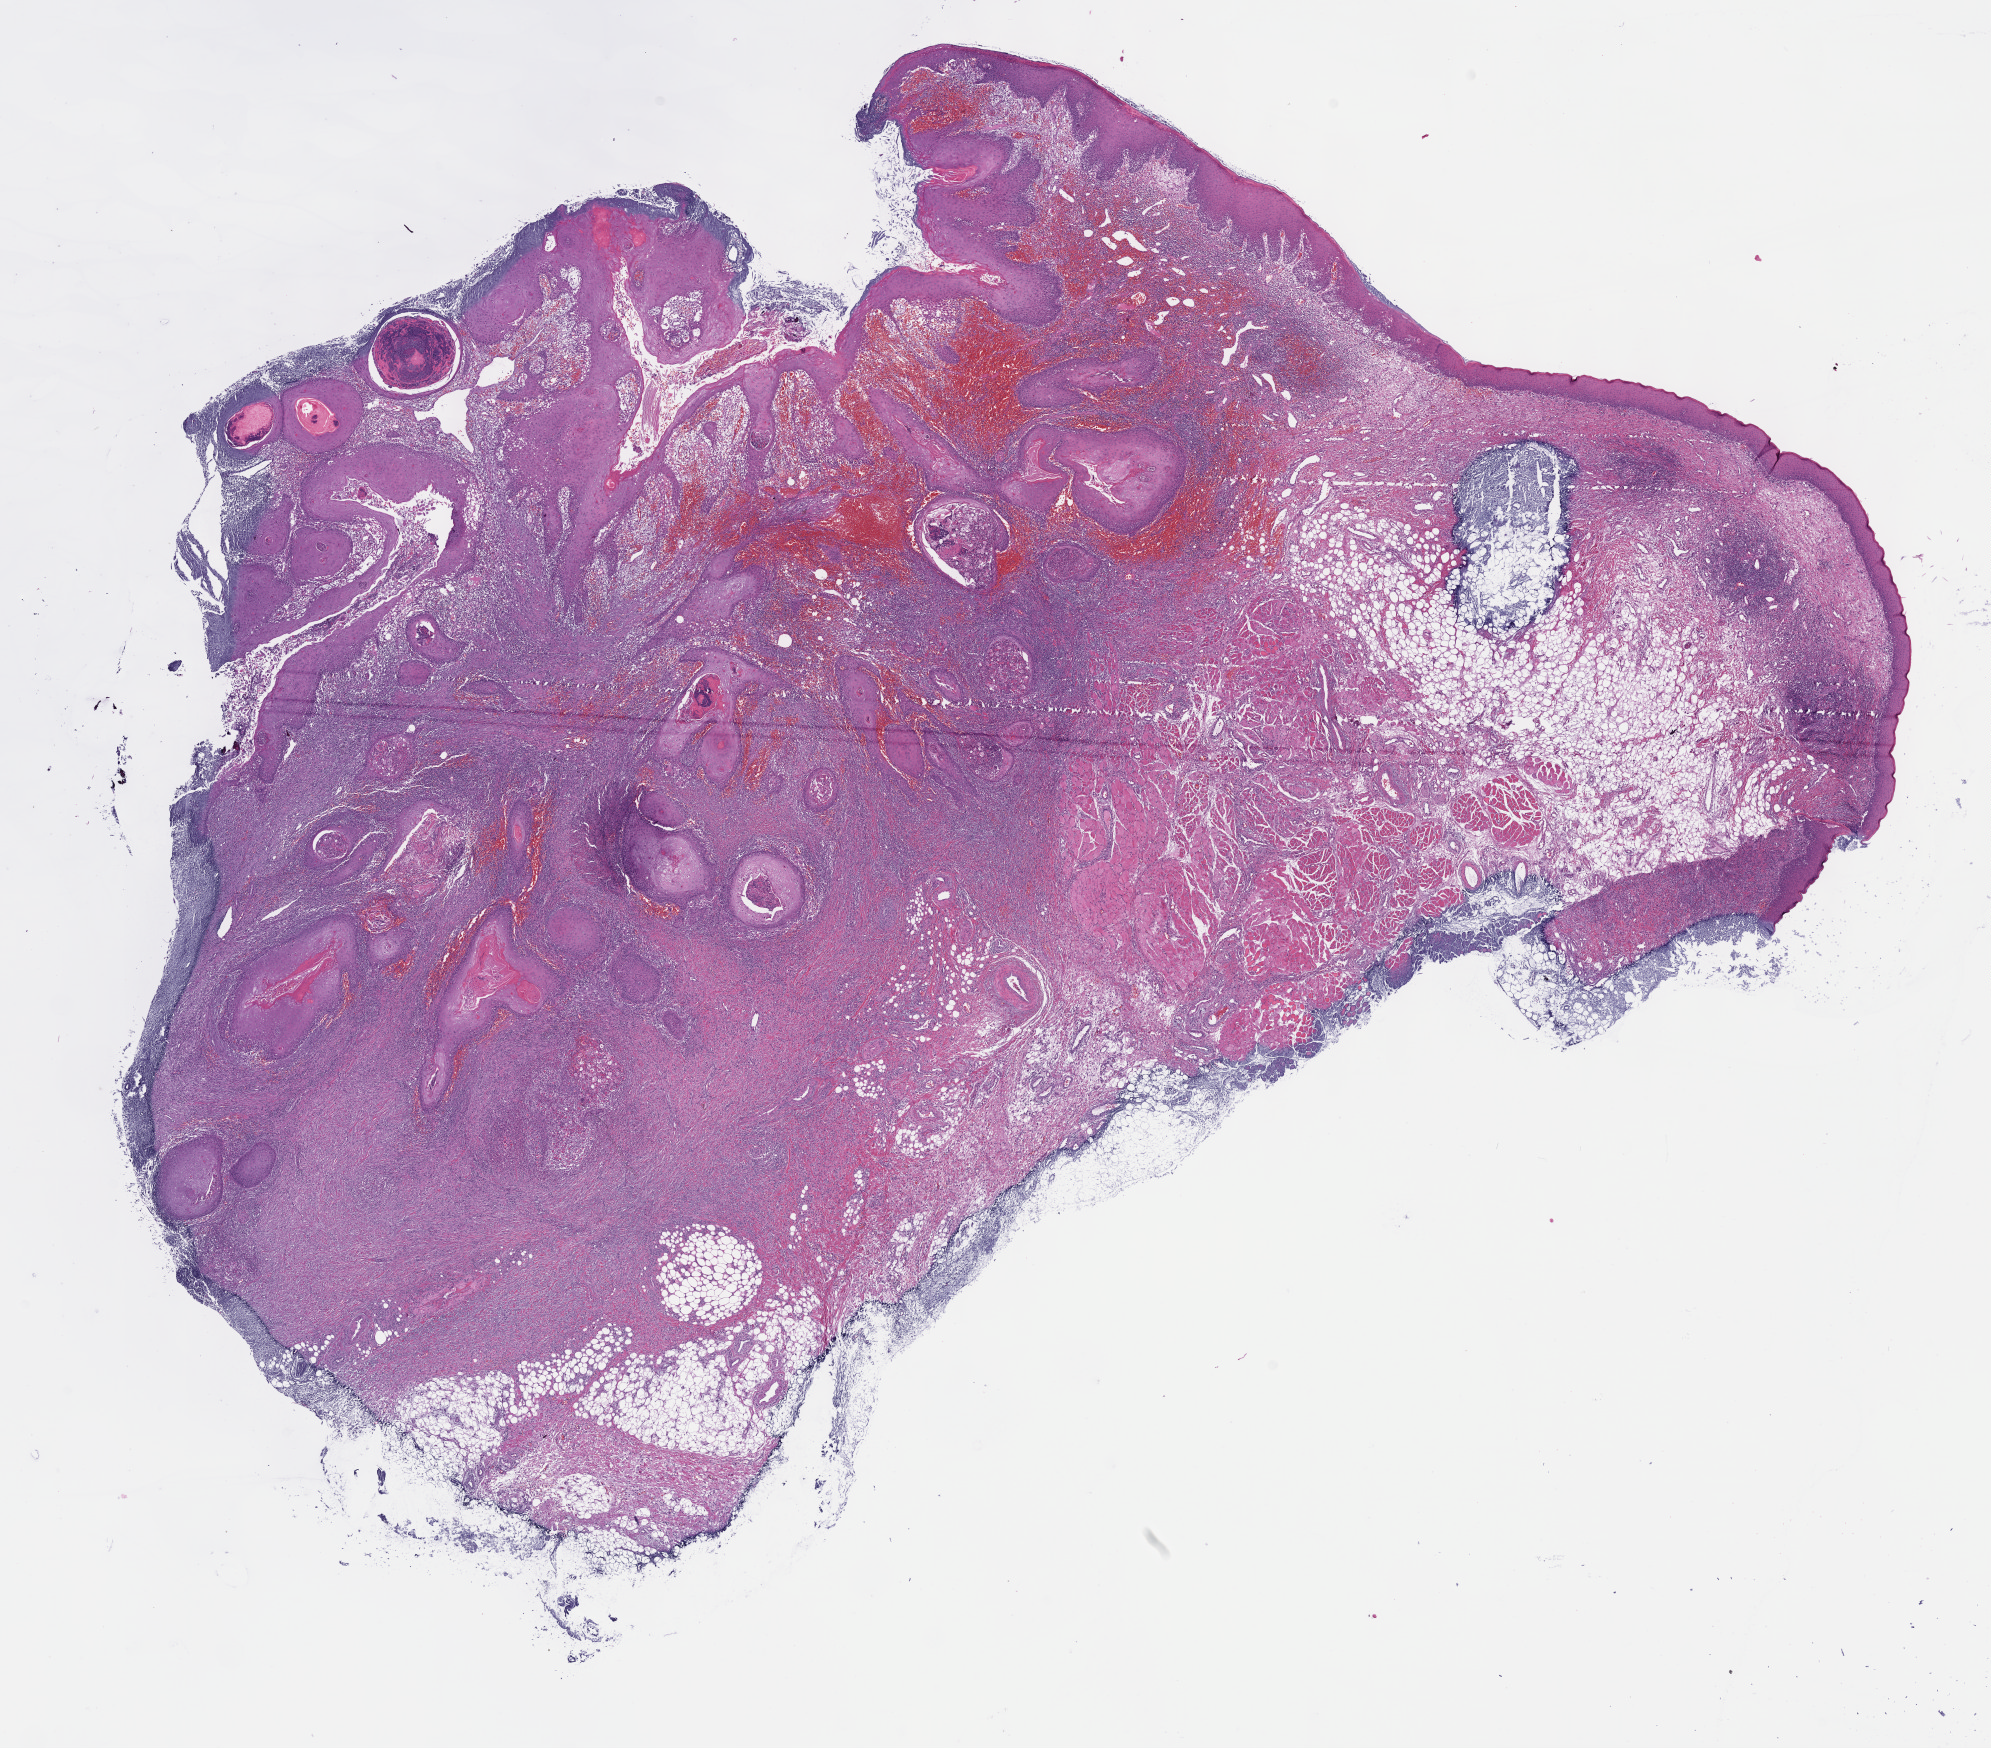
Digitized H&E tissue section (whole slide), a low-resolution overview of the entire scanned area, about 16.1 x 14.1 mm (slide scanned at 40x). Formalin-fixed paraffin-embedded (FFPE) diagnostic section. Primary tumour sample from the head and neck. Male patient; age at initial diagnosis 47 years. Histologic grade: G2 (moderately differentiated).
- histologic diagnosis: Squamous cell carcinoma, NOS
- AJCC pathologic stage: IVA (5th edition)